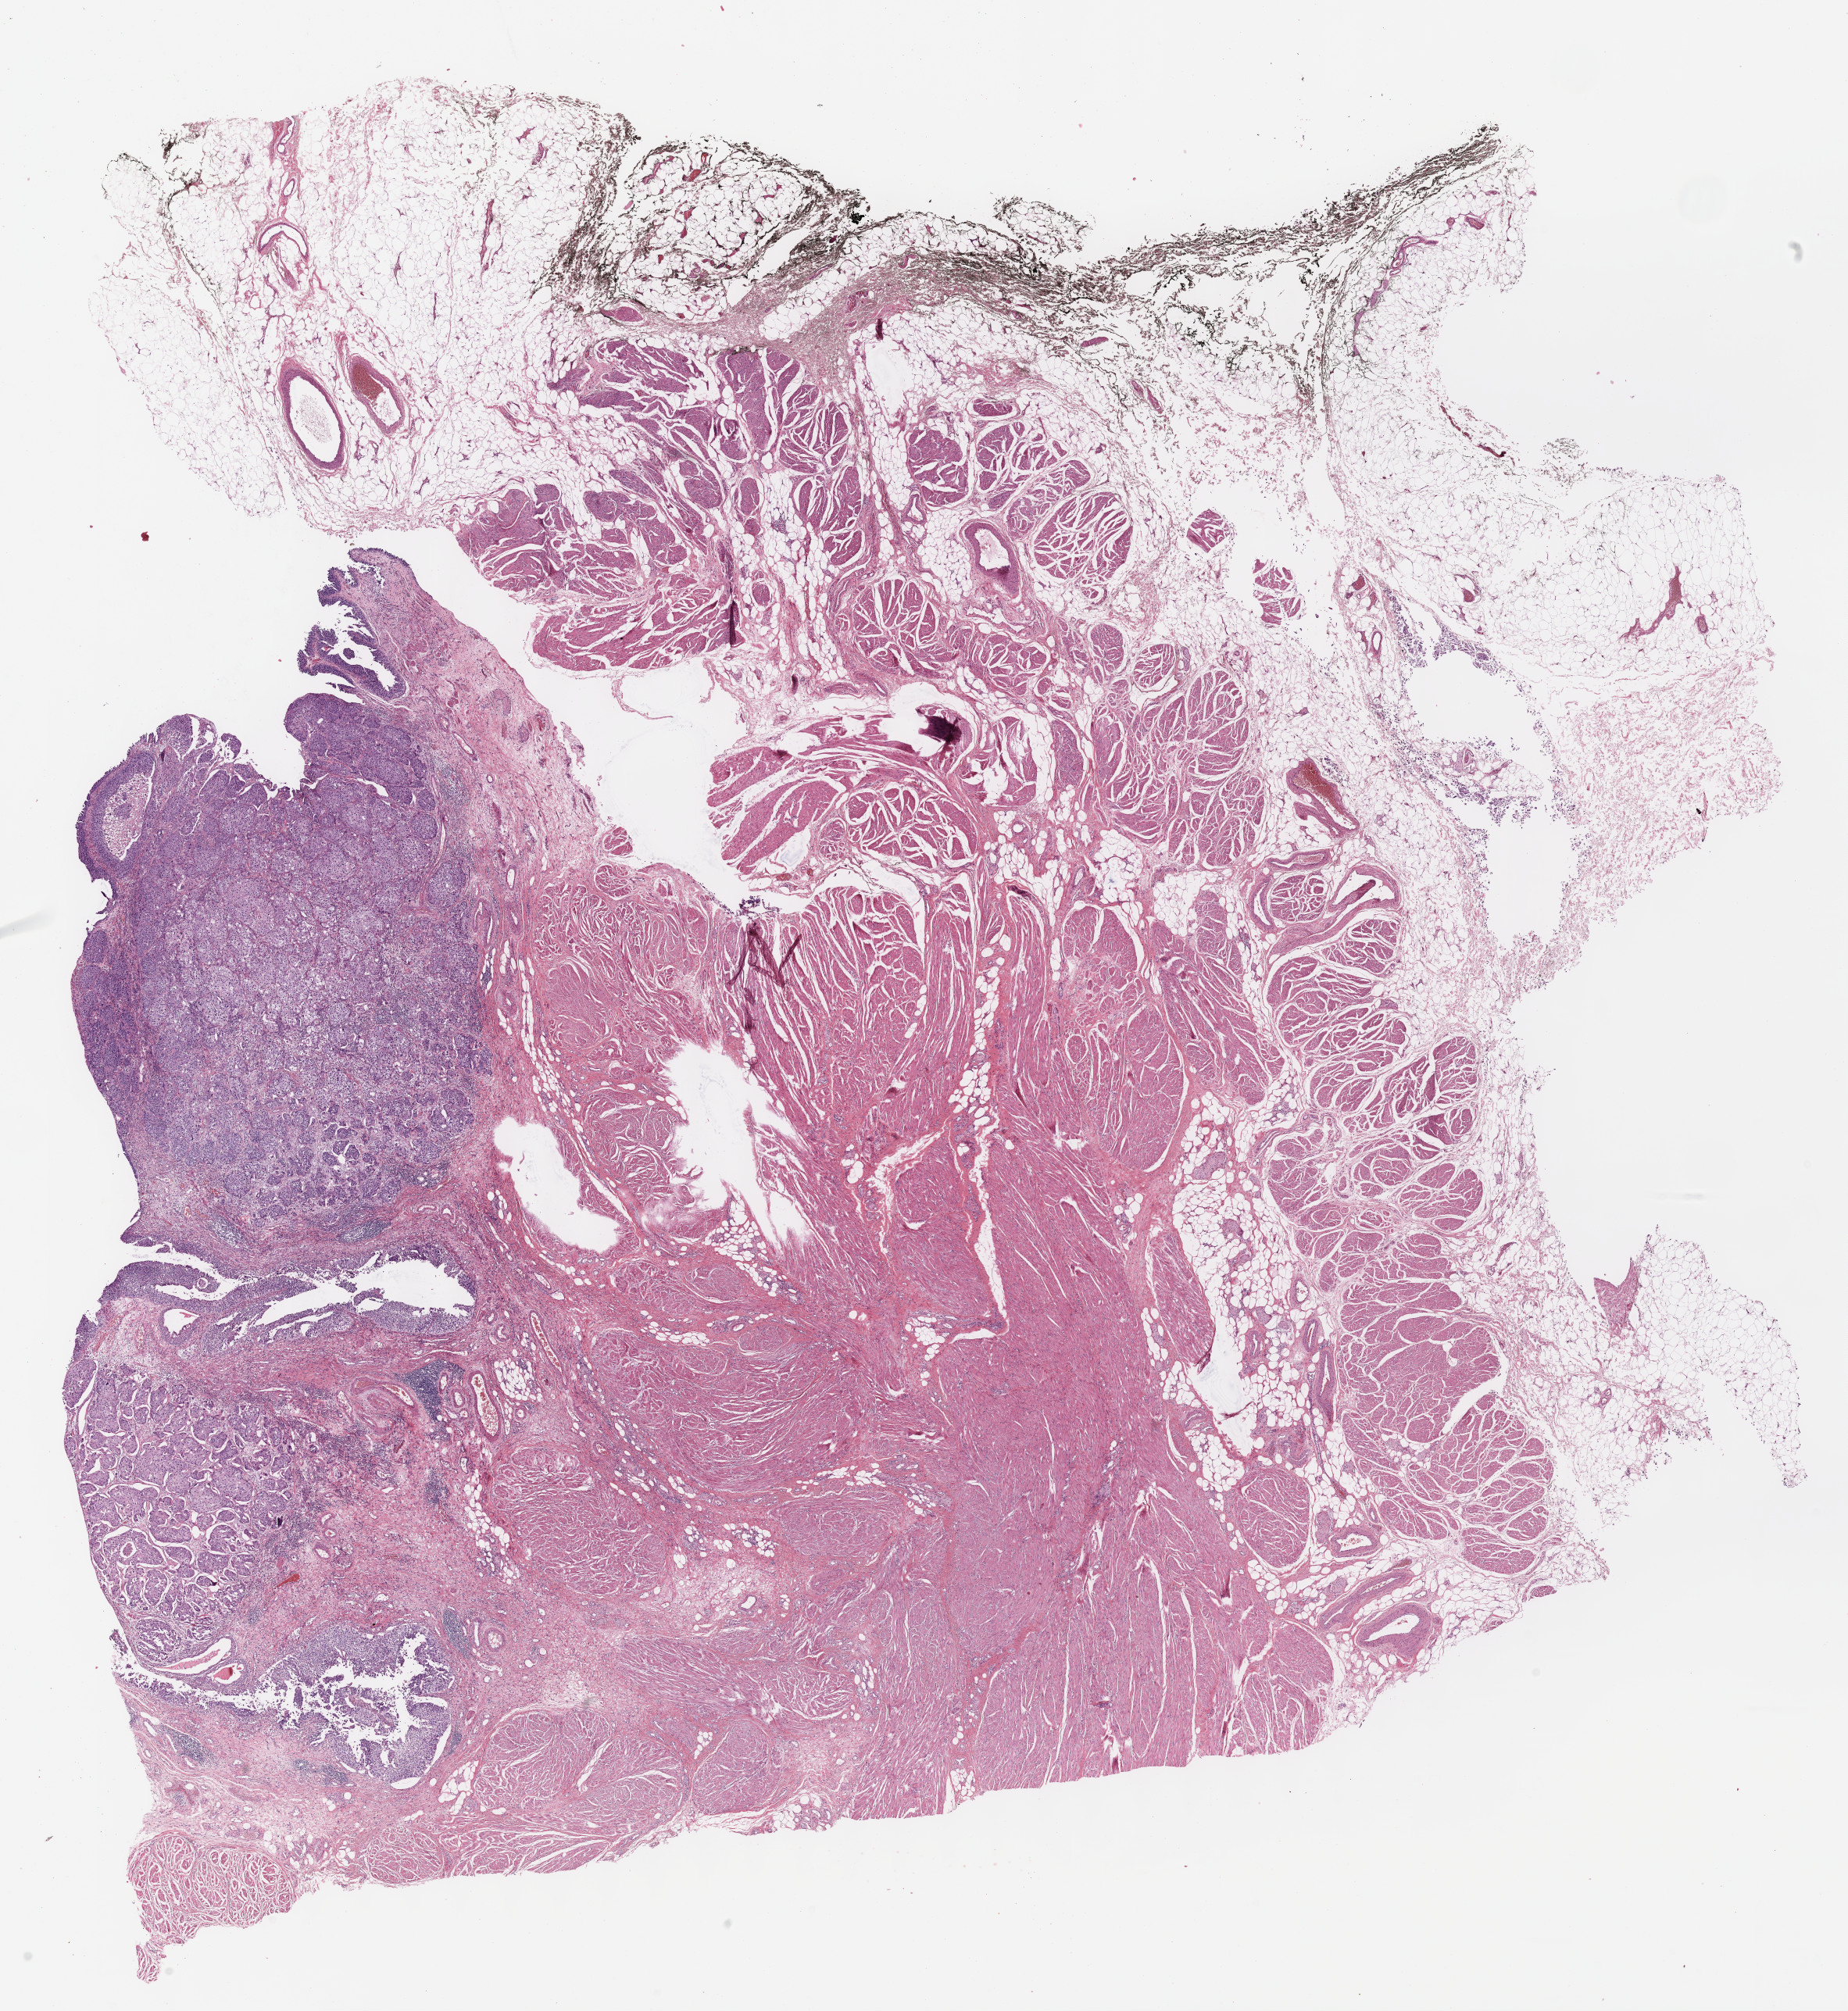
Whole-slide histology image, H&E-stained, shown as a low-resolution overview of the whole scanned area (about 19.1 x 20.8 mm); formalin-fixed paraffin-embedded (FFPE) diagnostic section; sample: primary tumour, bladder. Male, age 66 years at initial diagnosis. Histologic grade: high grade.
• TNM: T4a N0 M0
• AJCC pathologic stage: III (7th edition)
• pathologic diagnosis: Papillary transitional cell carcinoma
• lymph nodes positive (case pathology): 0 of 22 examined